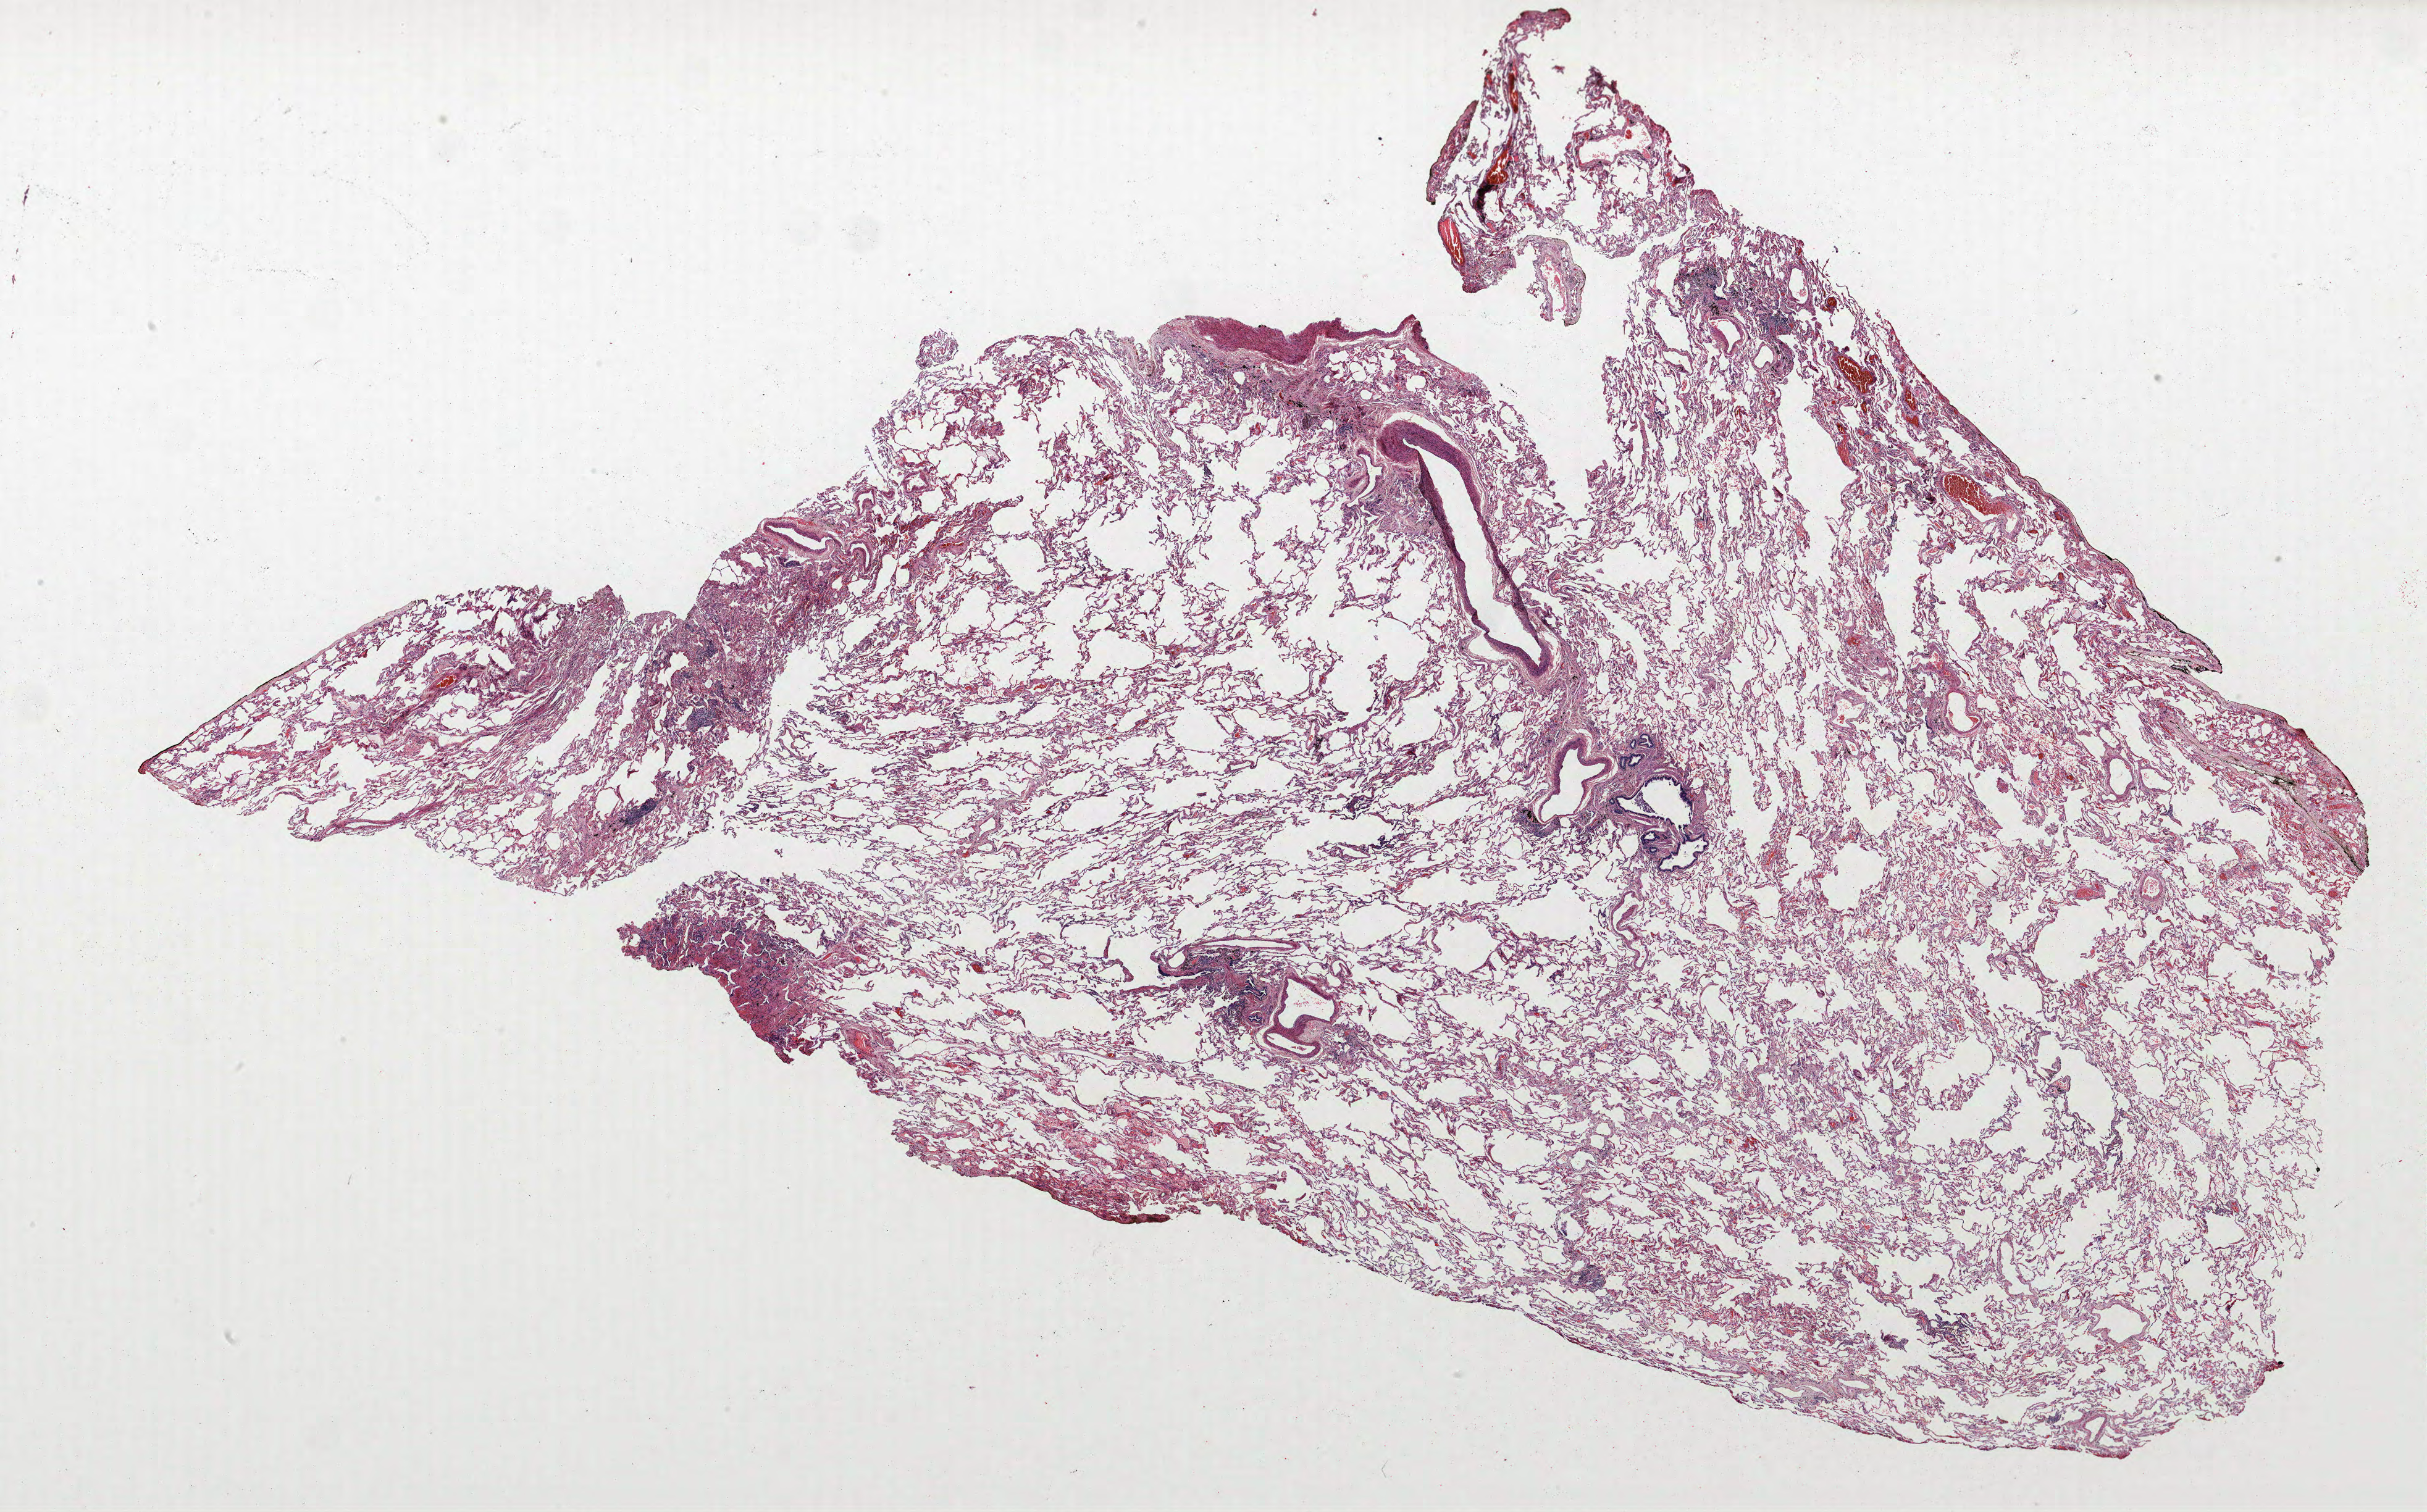
Whole-slide histology image, Hematoxylin and eosin (H&E) stained, low-resolution overview of the scanned area, about 31.4 x 19.6 mm, FFPE section, lung. Female patient, aged 68 at enrolment. Current smoker at enrolment.
ICD-O-3 topography: lower lobe of lung (C34.3). Stage (AJCC 6th edition): IIIB. Tumour size (pathology): 12 mm. Participant's lung-cancer diagnosis: Bronchiolo-alveolar adenocarcinoma, NOS. Primary tumour location (clinical record): left lower lobe.